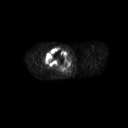
FDG PET of an extremity soft-tissue mass (from a PET/CT study), one axial slice. Position 256 of 311 along the scan axis. 128 × 128 image matrix. Male patient, age 50 years. Case-level facts recorded for this patient, not image findings: histological type: undifferentiated - pleiomorphic; grade: high; site of the primary tumour: right thigh.
Structures marked on this image (expert contour drawn on MRI and transferred to this co-registered scan by the dataset authors):
- gross tumour volume including surrounding oedema: bounding box <42,48,66,68> (left, top, right, bottom; pixels)
- gross tumour volume (mass): <45,48,66,67>